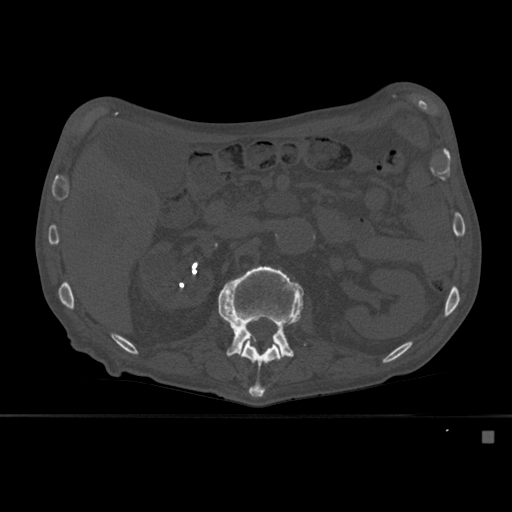
CT including the spine, one axial slice; position 244 of 527 along the scan axis; bone window (W 1800 / L 400 HU); 1.5 mm slice thickness; 512 × 512 image matrix, field of view 373 × 373 mm. Patient: male, 78 years. From the clinical record (not read from this slice): primary cancer: prostate.
Annotated regions visible in this slice (semi-automatically segmented with operator editing):
- L1 vertebra: box from (x=240, y=341) to (x=281, y=398) px
- L2 vertebra: (x=218, y=265)–(x=306, y=358)